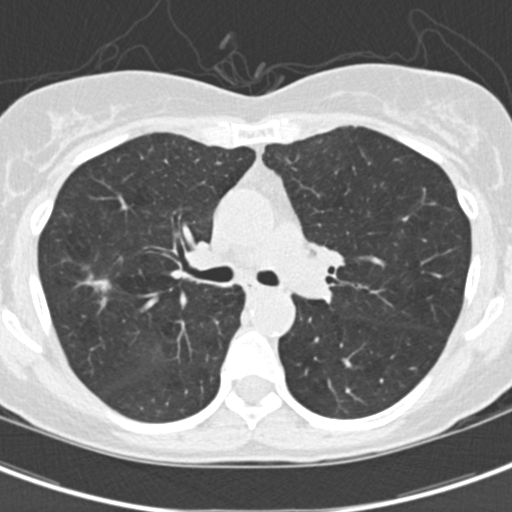
Low-dose screening chest CT, one axial slice; position 98 of 154 along the scan axis; lung window (W 1500 / L -600 HU); 512 × 512 image matrix.
Annotated regions visible in this slice (outlined manually by an expert reader):
- lesion 1 (tumor, upper lobe of right lung): bounding box [x1, y1, x2, y2] px = [84, 274, 111, 292]